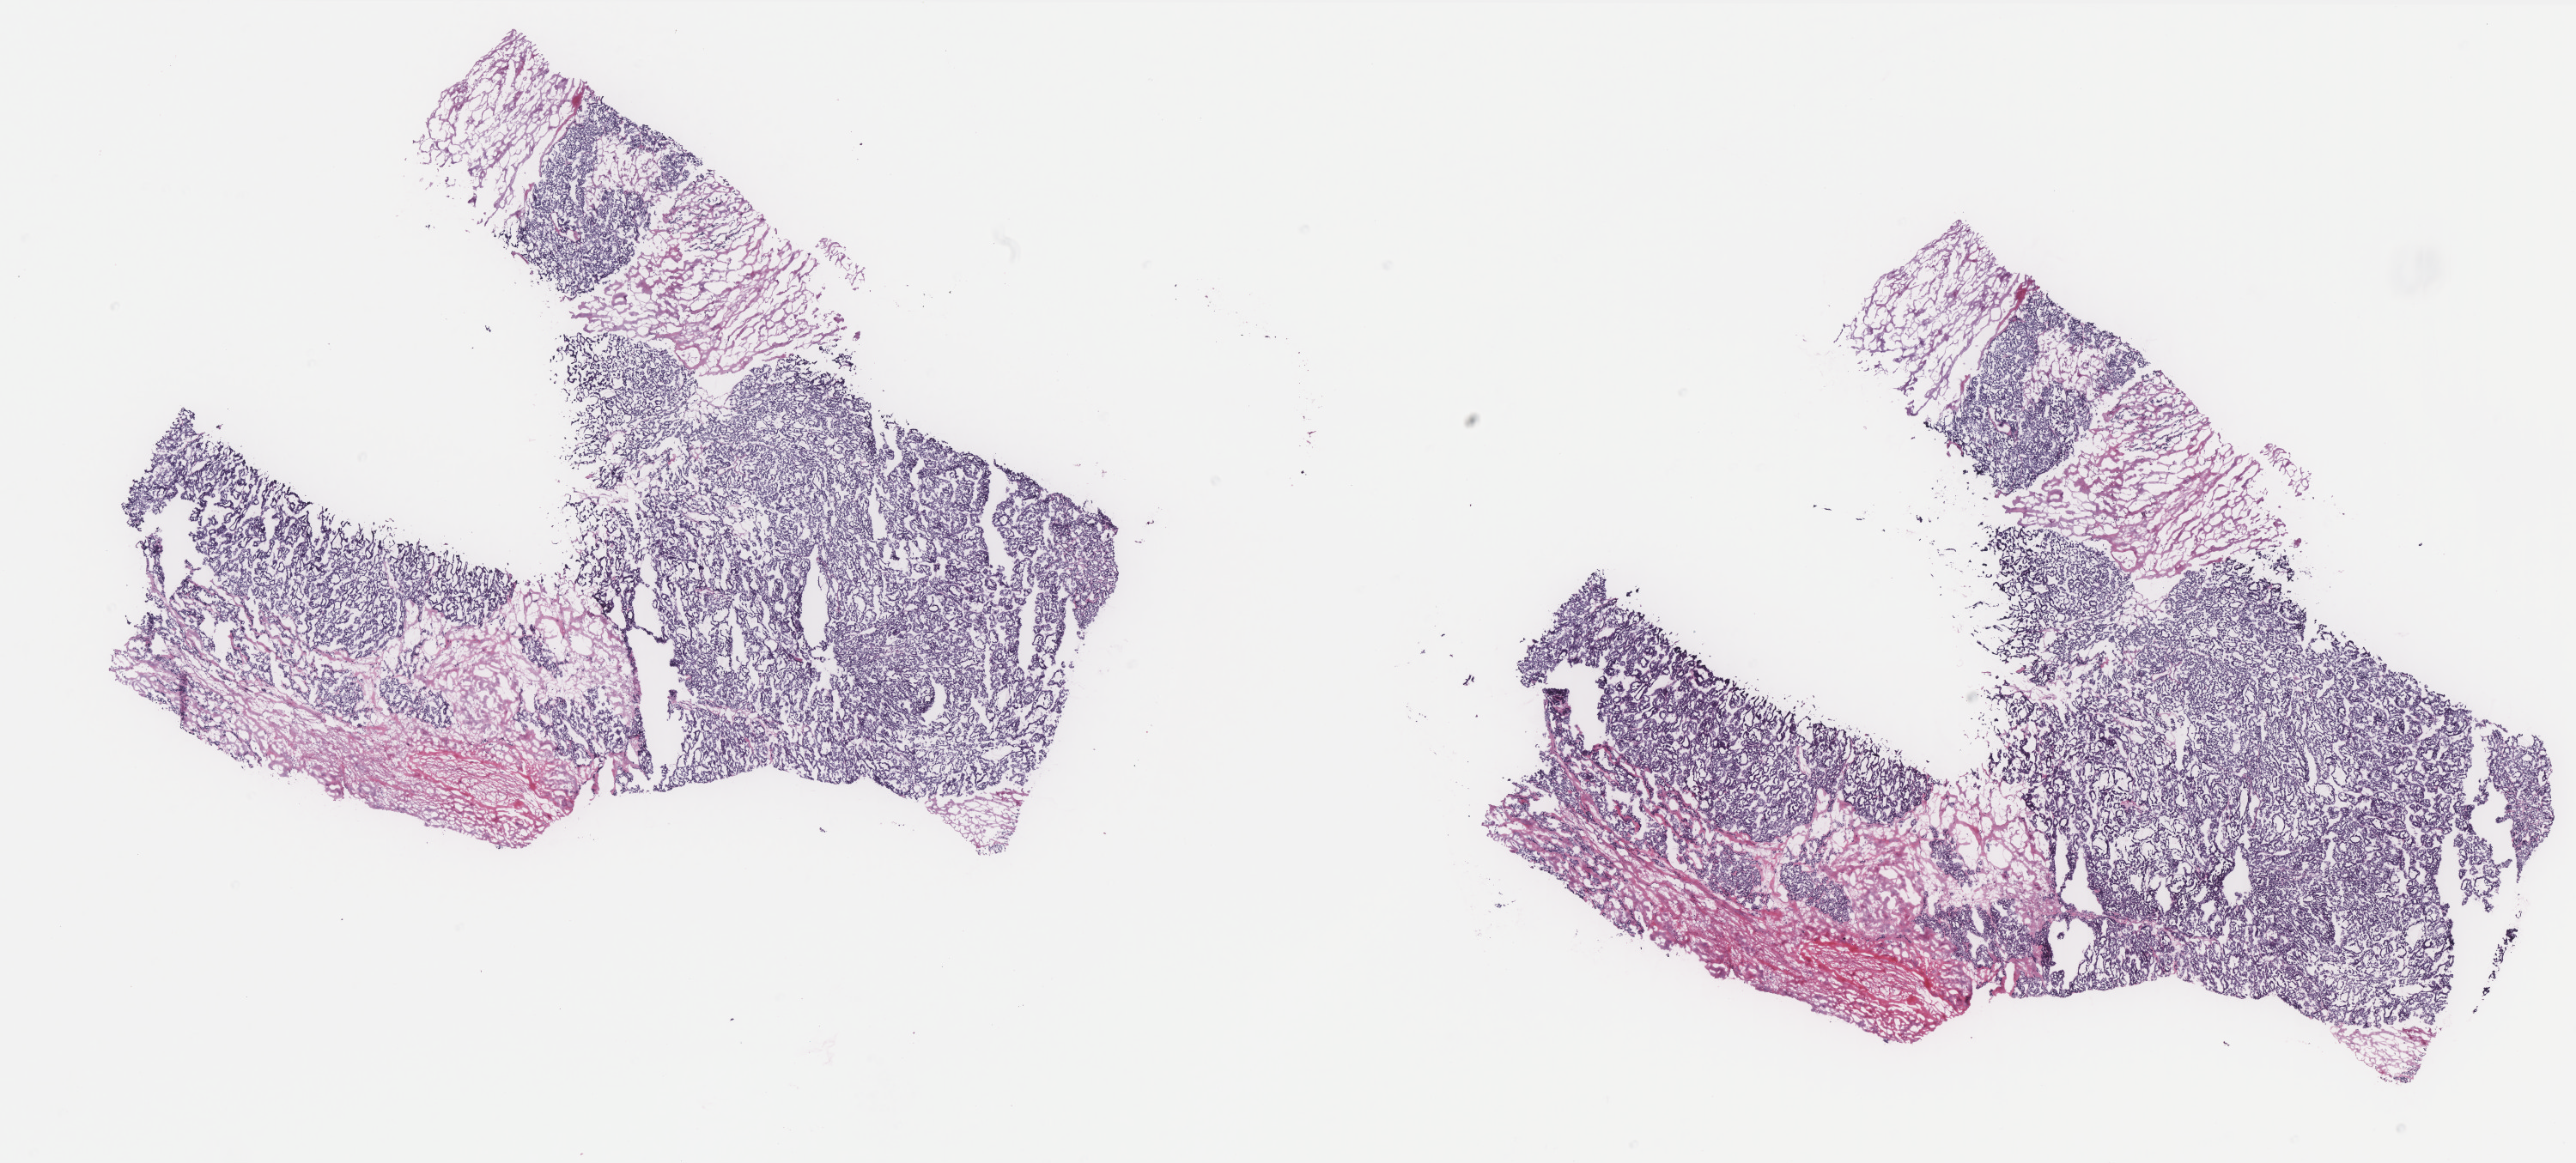
Whole-slide histology image, H&E-stained — low-resolution overview of the scanned area, about 24.1 x 10.9 mm (acquisition: 40x scan). Frozen section. Primary tumour sample from the thyroid. Male patient; age at initial diagnosis 57 years.
Diagnosis: Follicular adenocarcinoma, NOS (thyroid gland).